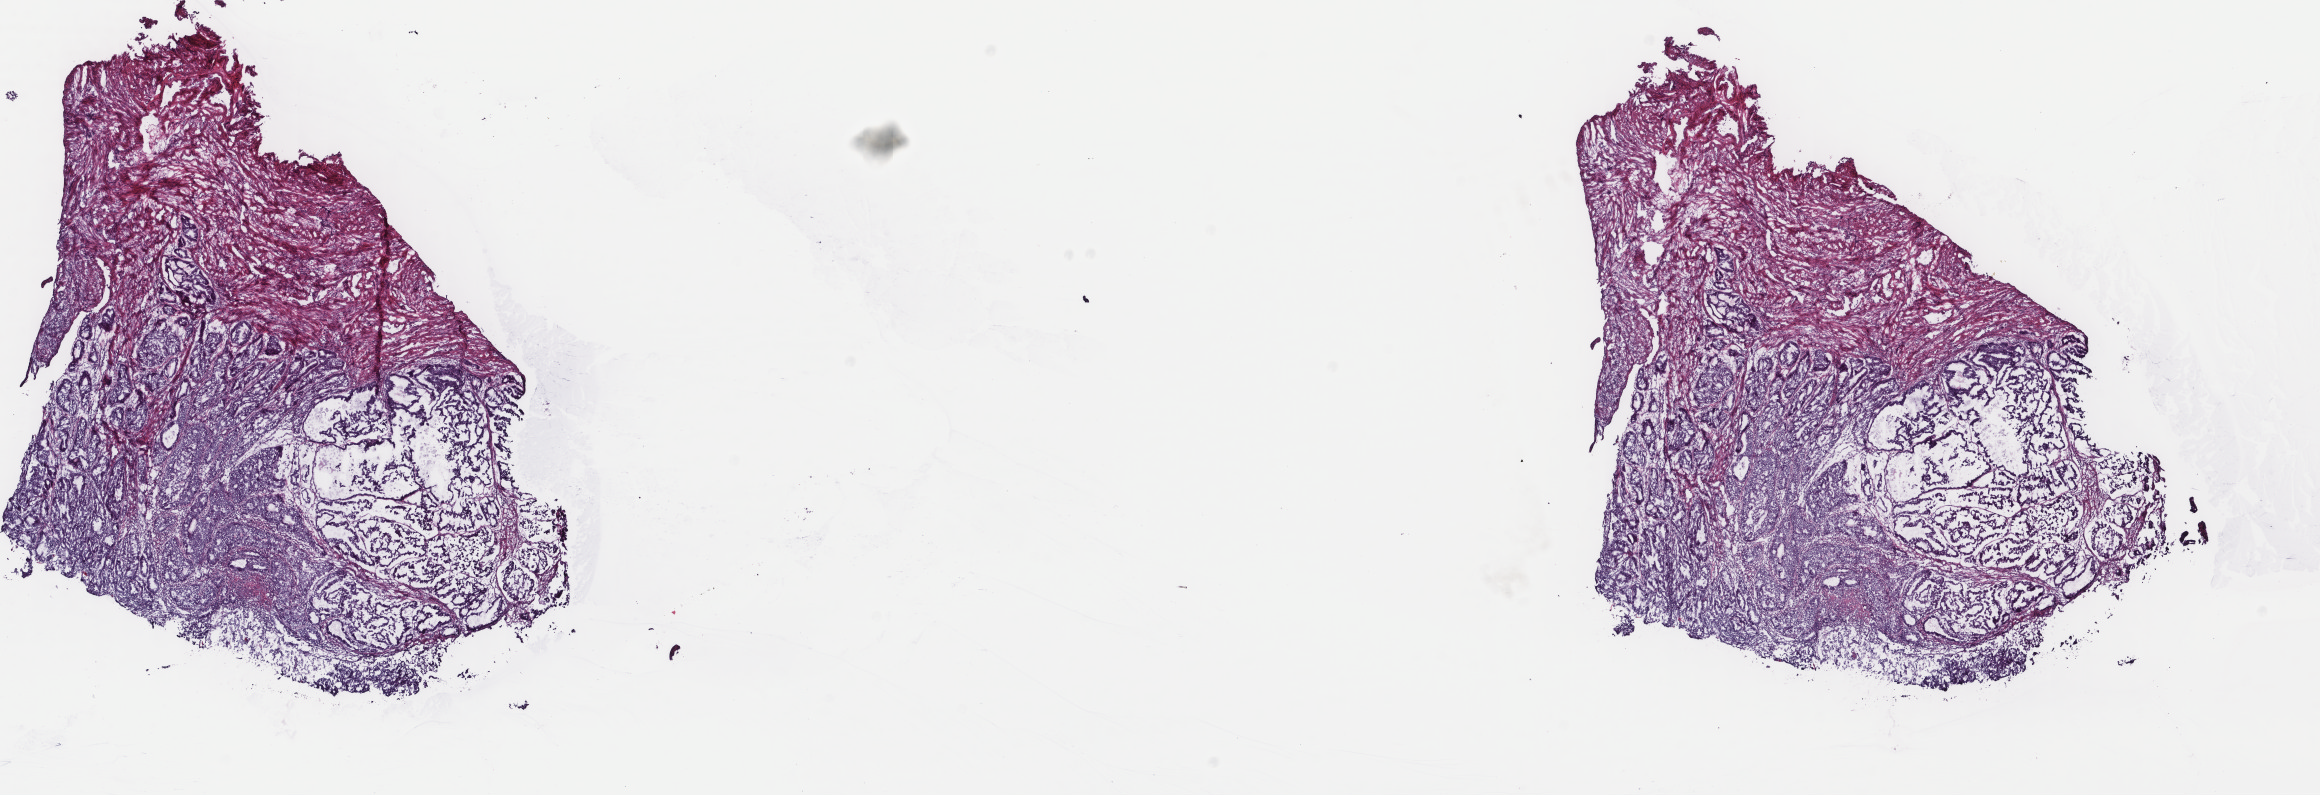
Digitized H&E-stained tissue section (whole slide) — whole scanned area (about 18.4 x 6.3 mm, slide scanned at 40x) shown as a low-resolution overview; frozen section from the top of the tissue portion; uterus, primary tumour sample. Patient: female, age at initial diagnosis 64 years. Histologic grade: G1 (well differentiated). Slide review estimates, as recorded: tumour cells 60%, tumour nuclei 60%, normal cells 0%, stromal cells 40%, necrosis 0%. Infiltration values recorded for this section: lymphocyte infiltration 4%, monocyte infiltration 1%, neutrophil infiltration 0%.
Lymph nodes positive (case pathology): 0 of 13 examined. Diagnosis: Endometrioid adenocarcinoma, NOS (endometrium). FIGO stage: IIIA.